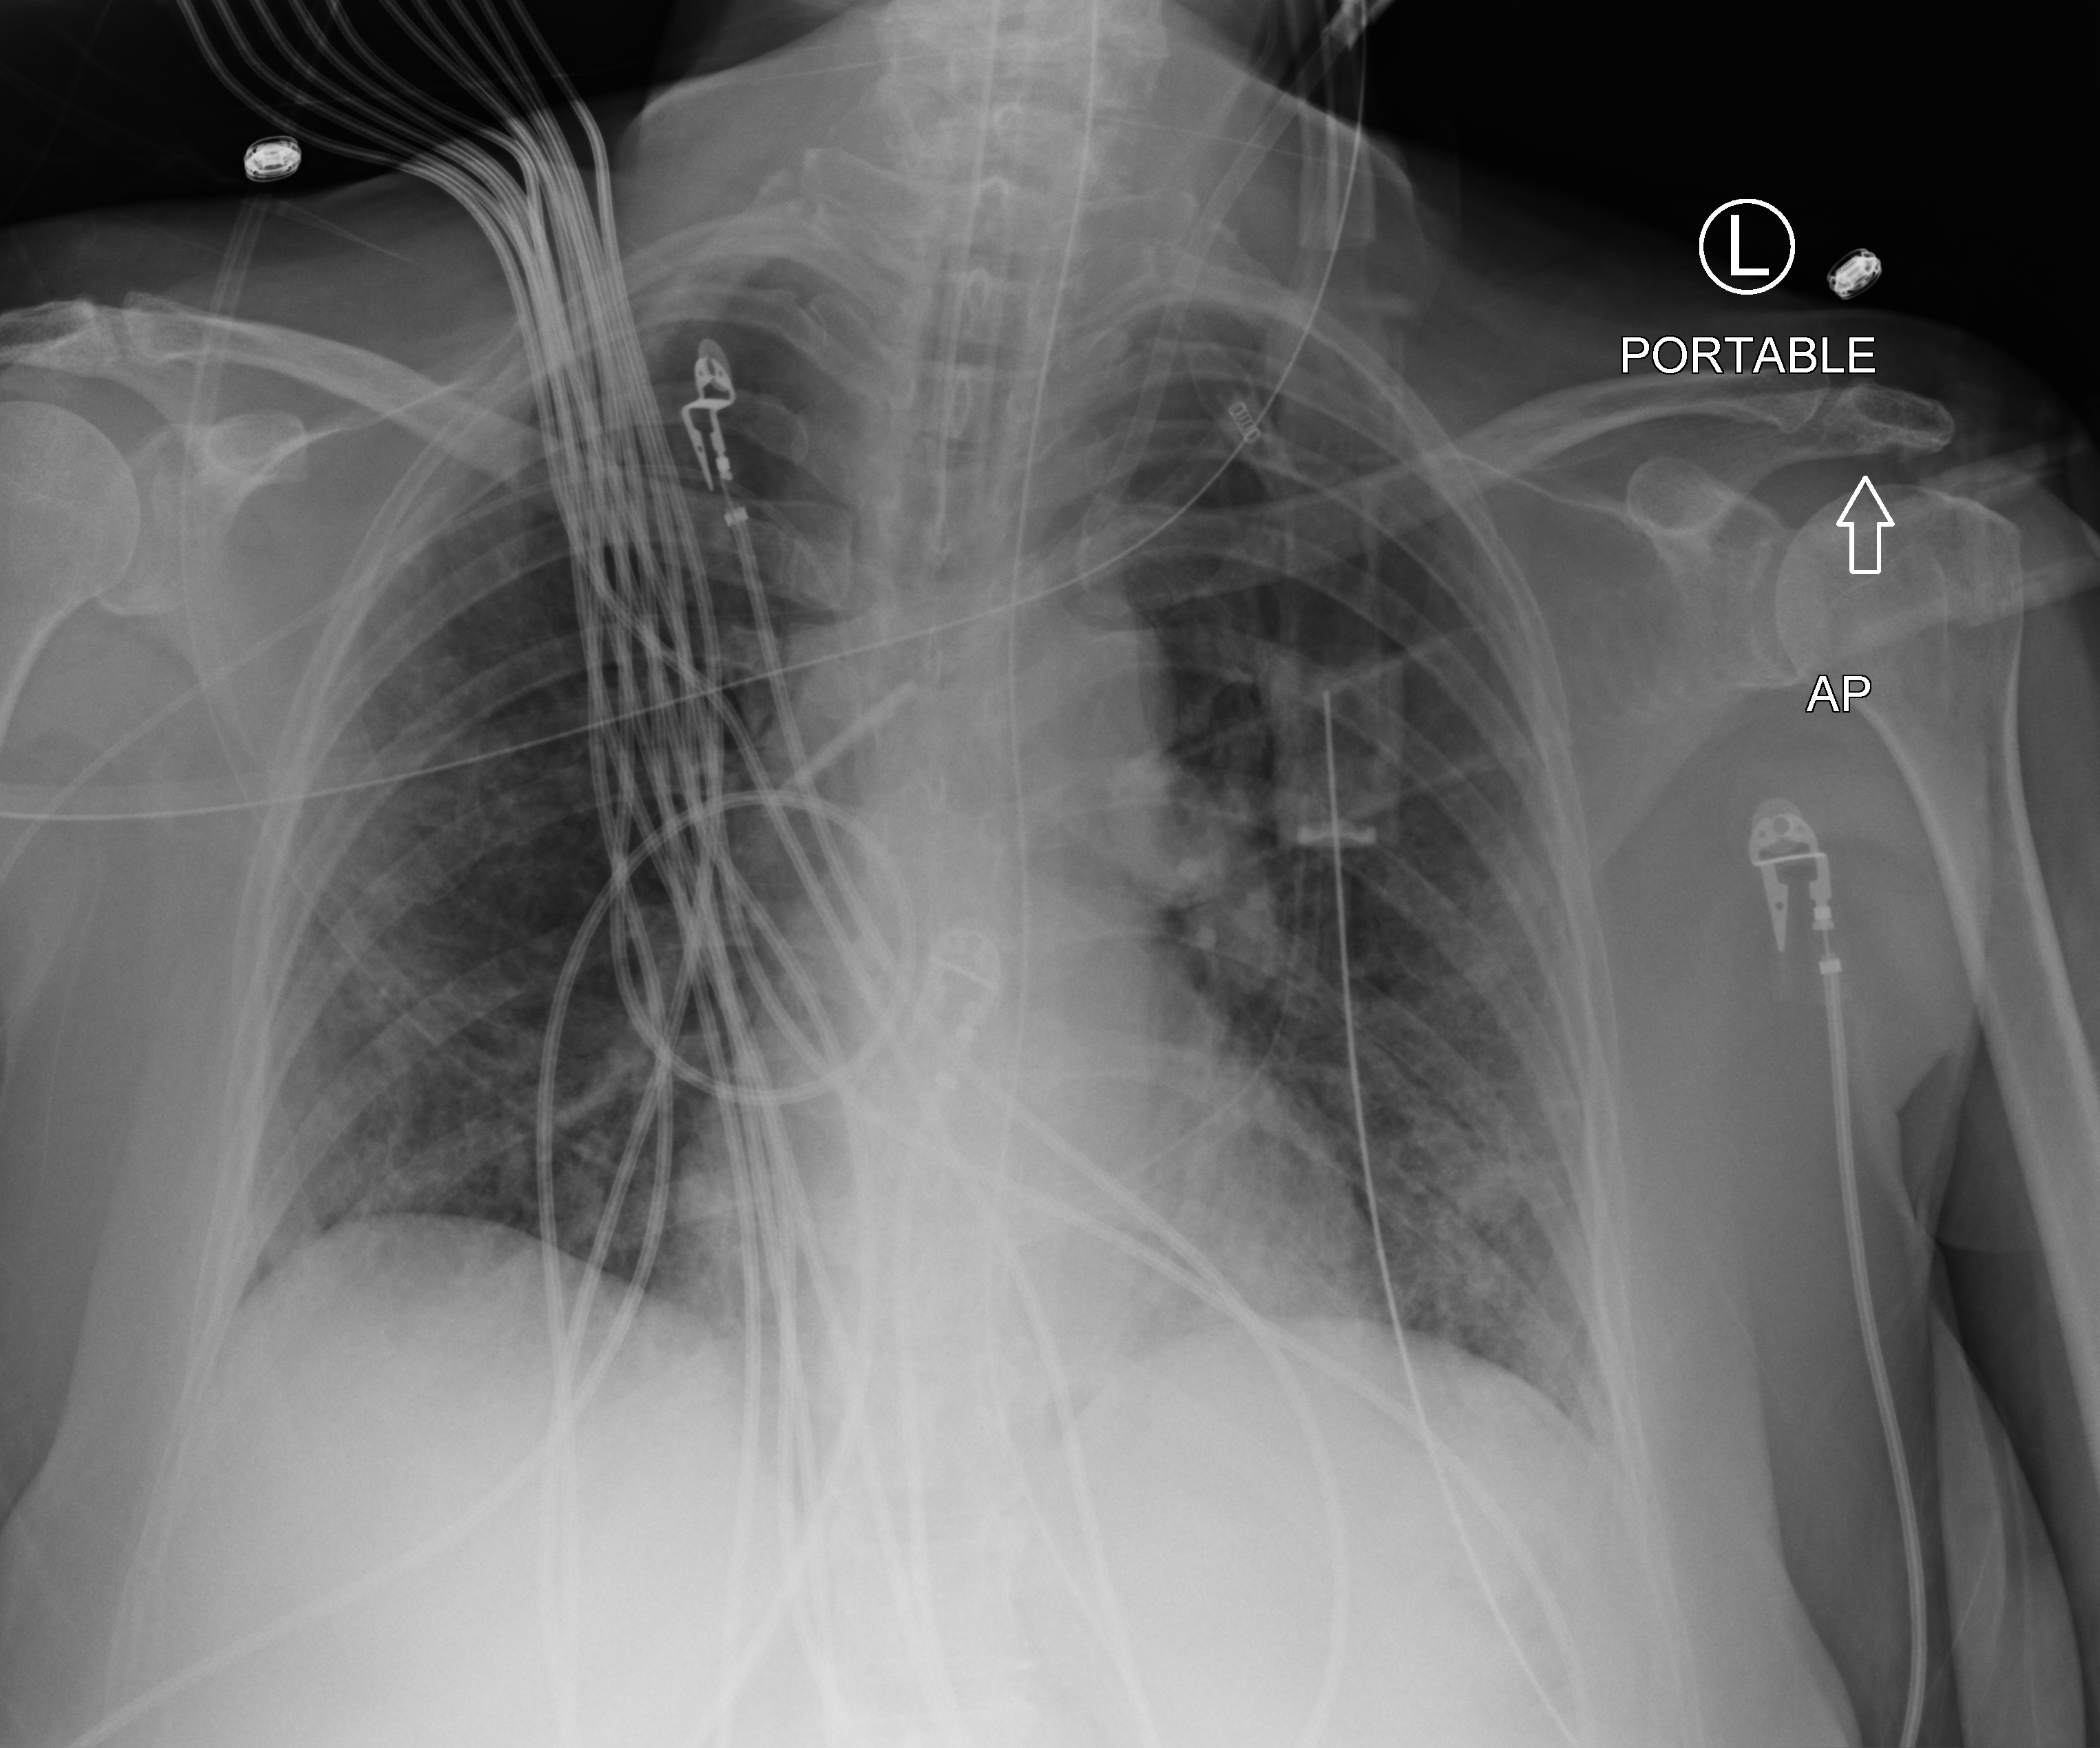
Chest X-ray (portable); anteroposterior (AP) projection. Female patient hospitalised with COVID-19, age 60–74 years.
Admission-level facts for this patient (not findings on this image; timing relative to this image not recorded):
- admitted to intensive care during this hospital stay: yes
- mechanically ventilated during this hospital stay: yes
- length of hospital stay: 43 days